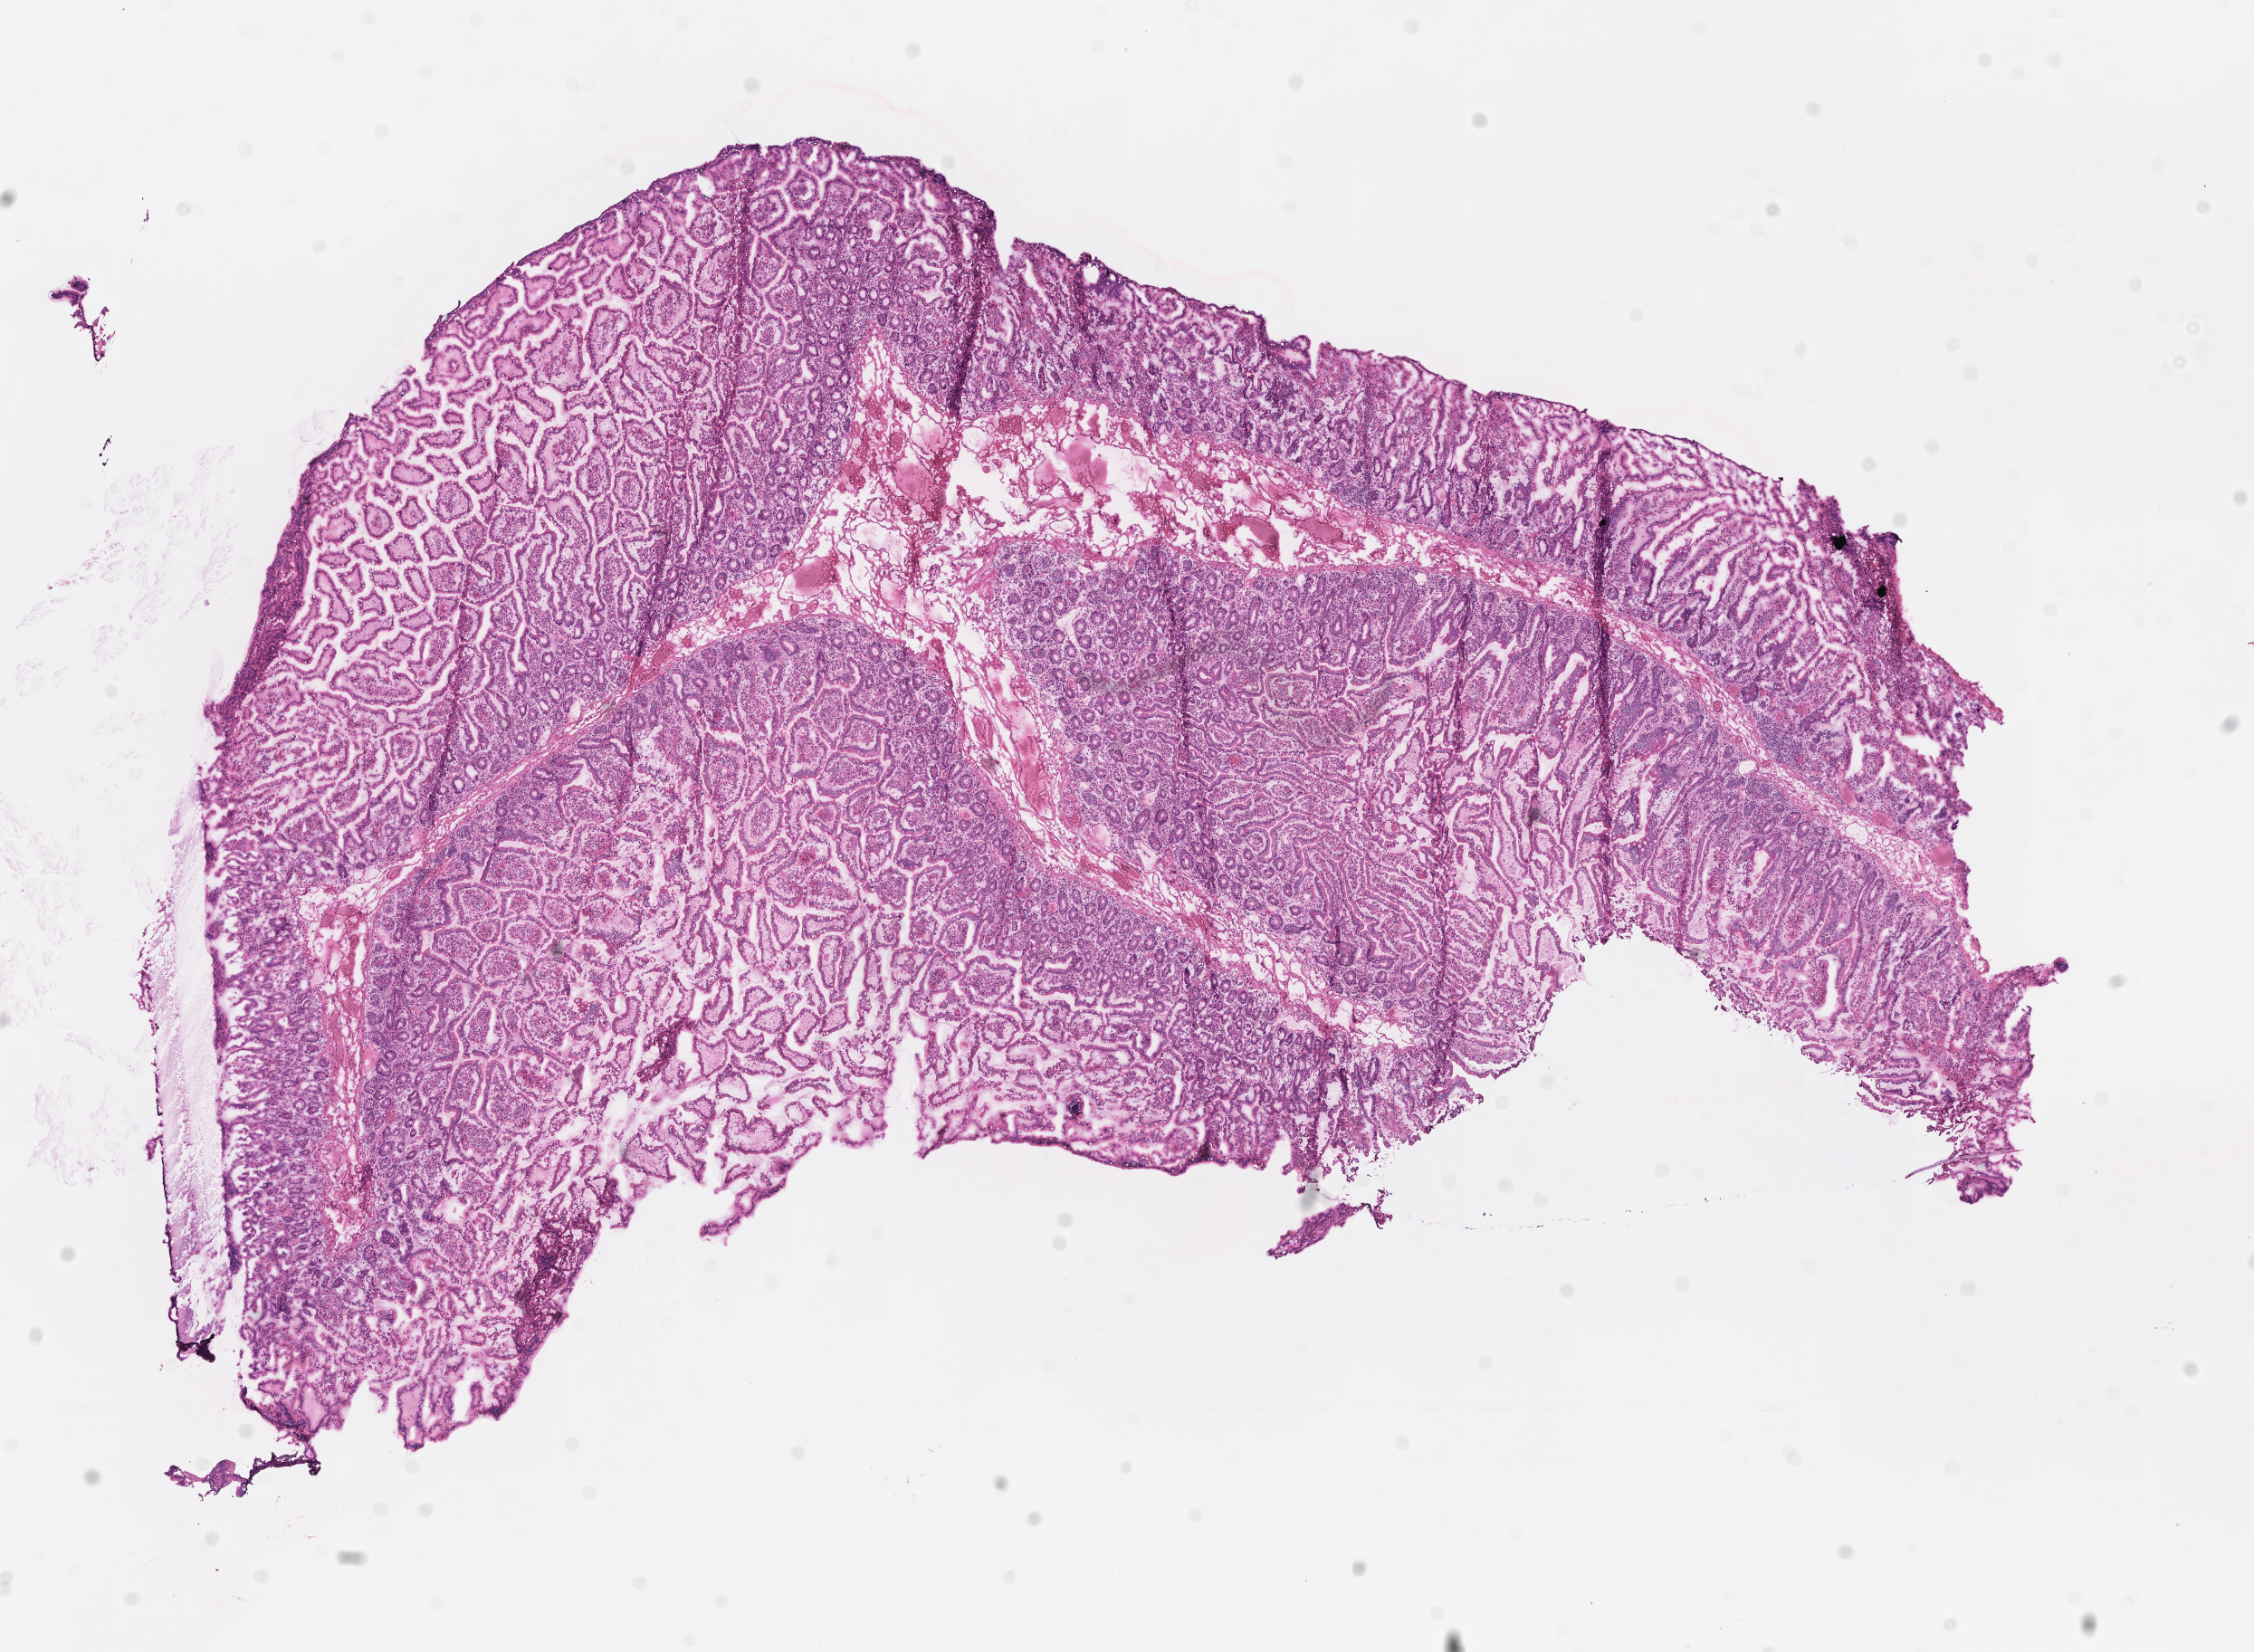
Digitized hematoxylin and eosin (H&E)-stained section — shown as a low-resolution overview of the whole scanned area (about 10.1 x 7.4 mm), frozen section, specimen: non-tumor (normal tissue) sample from a patient with adenocarcinoma, metastatic, NOS. Male, age 58 years at initial diagnosis.
This section: non-tumor tissue sample; the patient's diagnosis is given above.